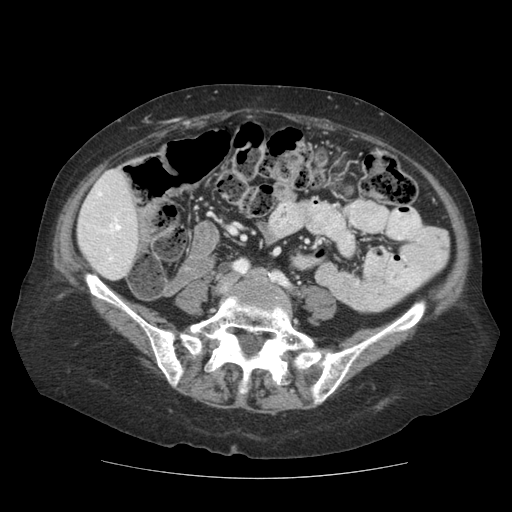
Contrast-enhanced abdominal CT (liver protocol), one axial slice. Position 24 of 111 along the scan axis. Soft-tissue window (W 400 / L 40 HU). 2.5 mm slice thickness. 512 × 512 image matrix, field of view 360 × 360 mm. Case-level facts recorded for this patient, not image findings: diagnosis: hepatocellular carcinoma (patient treated with transarterial chemoembolisation; whether this scan precedes or follows treatment is not stated here); TNM stage (as recorded): Stage-I; Child-Pugh class: A; tumour differentiation: moderately-poorly differentiated; tumour nodularity: uninodular.
Structures marked on this image (semi-automatically segmented with operator editing):
- liver parenchyma outside the tumour (the mass and vessels are separate outlines, so this box may not span the whole liver): box from (x=76, y=170) to (x=138, y=280) px
- liver vessels: (x=97, y=191)–(x=121, y=261)